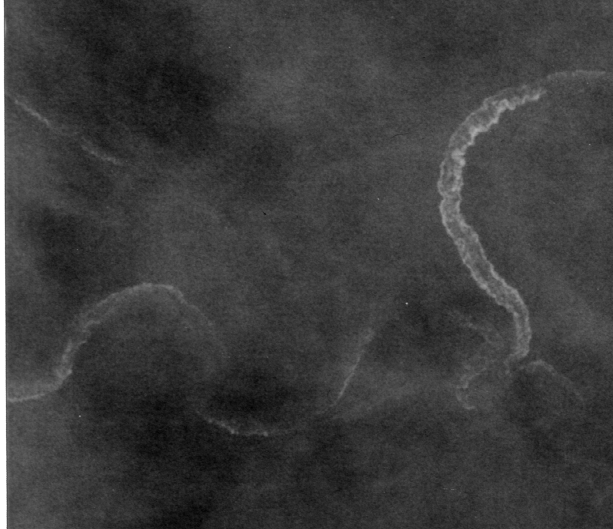
Crop from a digitized film mammogram around one marked abnormality; left breast; CC view; BI-RADS breast density category 4 (scale 1–4).
Finding: calcifications, morphology vascular; BI-RADS assessment category 2; subtlety rating 5 on a 1 (subtle) to 5 (obvious) scale; benign without callback (not worked up further).